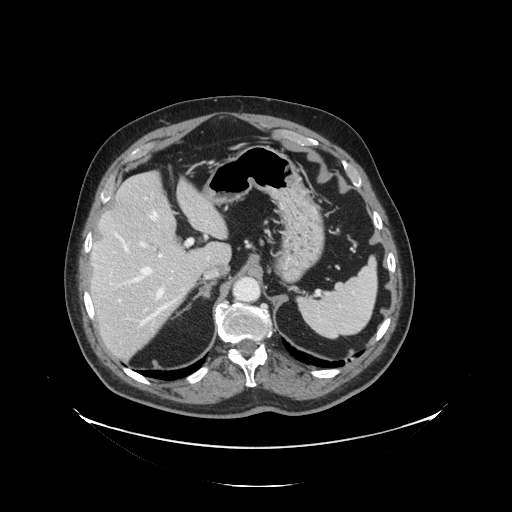
Contrast-enhanced abdominal CT, one axial slice; position 93 of 138 along the scan axis; reconstruction kernel STANDARD; intravenous contrast given; soft-tissue window (W 400 / L 40 HU); 2.5 mm slice thickness; 512 × 512 image matrix, field of view 497 × 497 mm. Male patient, age 77 years. From the clinical record (not read from this slice): diagnosis: colorectal cancer liver metastases, imaged before liver resection; multiple liver metastases: no; largest metastasis: 1.5 cm.
Annotated regions visible in this slice (expert manual segmentation):
- hepatic veins: bounding box [x1, y1, x2, y2] px = [115, 211, 176, 326]
- liver: [92, 173, 231, 360]
- planned liver remnant (the part of the liver to remain after resection): [92, 173, 229, 288]
- portal vein (with intrahepatic branches): [117, 239, 193, 302]